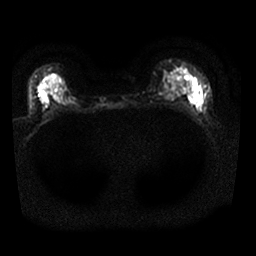
Breast MRI, one axial slice; position 18 of 25 along the scan axis; diffusion-weighted series; image 2 of 4 stored at this slice position (different b-values; order by instance number); 1.5 T; 4 mm slice thickness; 256 × 256 image matrix, field of view 320 × 320 mm. Female patient.
Annotated regions visible in this slice (manually delineated by an expert):
- tumour on diffusion-weighted imaging: bounding box [x1, y1, x2, y2] px = [187, 93, 201, 105]